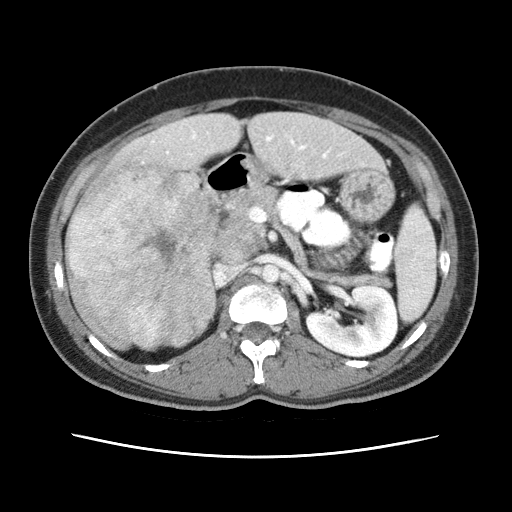
Contrast-enhanced abdominal CT (liver protocol), one axial slice; slice 22 of 79 in the series (ordered by position); 120 kVp; soft-tissue window (W 400 / L 40 HU); 512 × 512 image matrix, field of view 340 × 340 mm. From the clinical record (not read from this slice): diagnosis: hepatocellular carcinoma (patient treated with transarterial chemoembolisation; whether this scan precedes or follows treatment is not stated here); TNM stage (as recorded): Stage-I; Child-Pugh class: A; tumour differentiation: moderately differentiated.
Structures marked on this image (semi-automatically segmented with operator editing):
- abdominal aorta: box from (x=262, y=265) to (x=281, y=283) px
- liver parenchyma outside the tumour (the mass and vessels are separate outlines, so this box may not span the whole liver): (x=66, y=112)–(x=380, y=348)
- mass: (x=65, y=160)–(x=218, y=349)
- liver vessels: (x=152, y=134)–(x=329, y=158)